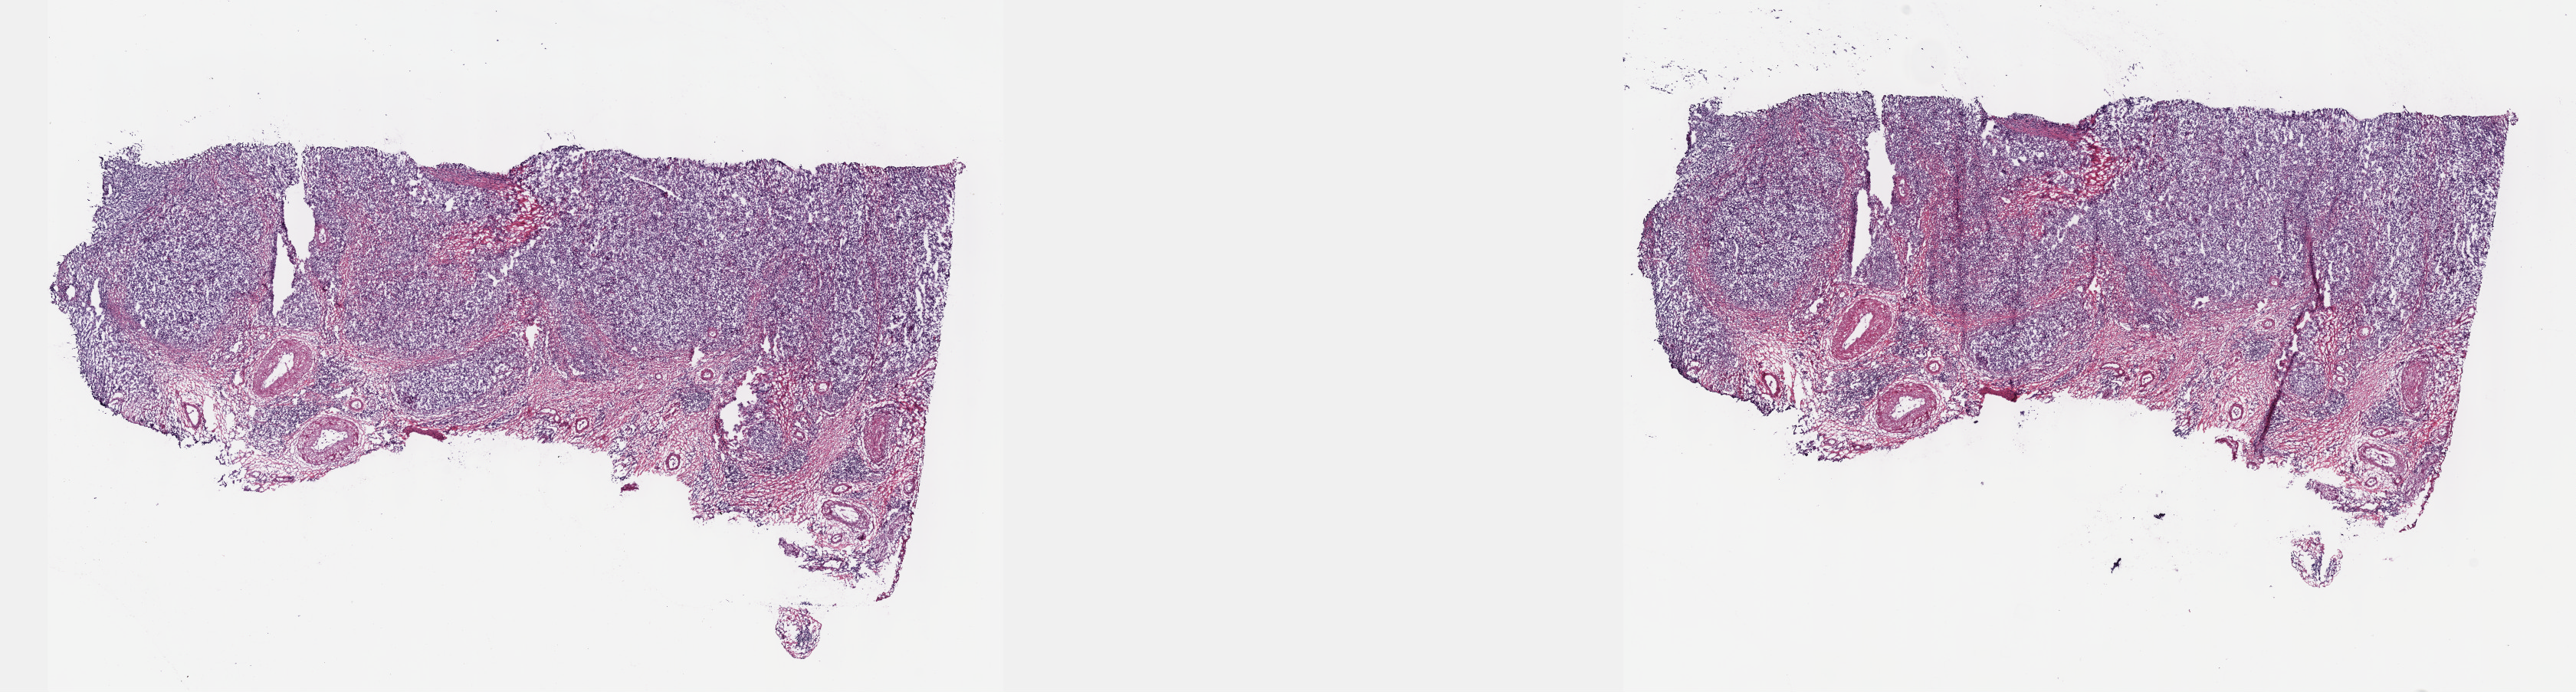
H&E whole-slide image — shown as a low-resolution overview of the whole scanned area (about 27.2 x 7.3 mm), frozen section from the top of the tissue portion, primary tumour sample from the lymphoid tissue. Female patient; age at initial diagnosis 48 years. Pathologist review of this section (percent, as recorded): tumour cells 90%, tumour nuclei 90%, normal cells 0%, stromal cells 5%, necrosis 5%. Inflammatory infiltration, as recorded: lymphocyte infiltration 75%, monocyte infiltration 10%, neutrophil infiltration 5%.
Diagnosis: Diffuse large B-cell lymphoma, NOS (small intestine, NOS).